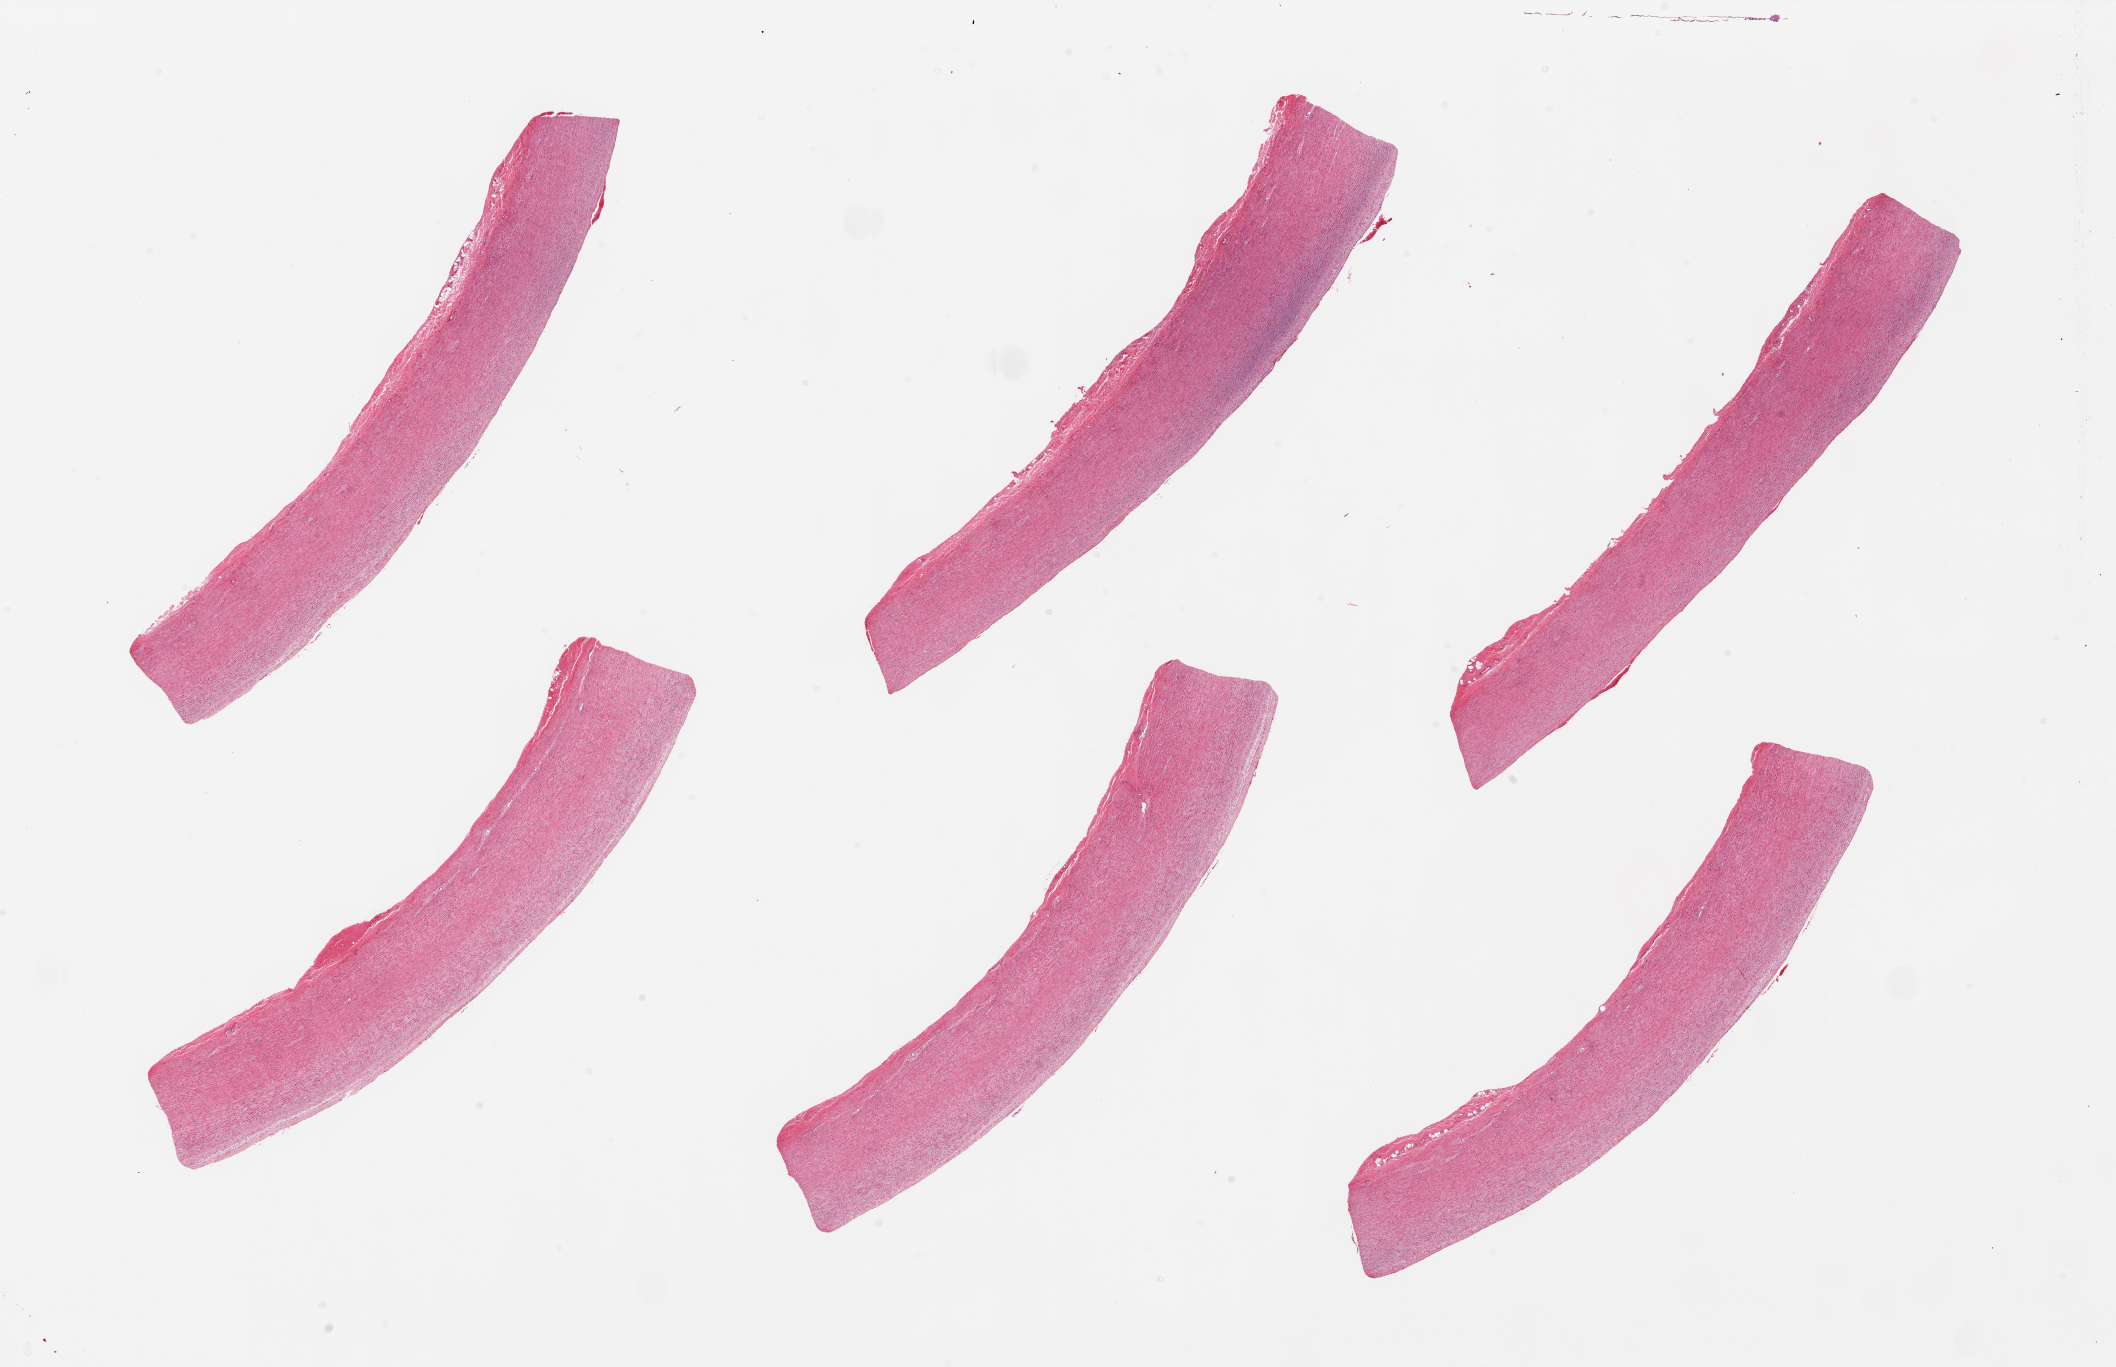
Whole-slide image, hematoxylin and eosin (H&E) stain, brightfield — whole scanned area (about 33.5 x 21.6 mm, slide scanned at 20x) shown as a low-resolution overview; PAXgene-fixed, paraffin-embedded tissue; sampled site (target tissue): aorta; tissue donor sample. Male donor.
Pathologist's review note for this sample: 6 pieces; well trimmed; no plaques.